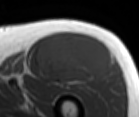
MRI of an extremity soft-tissue mass, one axial slice. Position 62 of 86 along the scan axis. MR volume resampled by the dataset authors to the PET/CT grid (not the native acquisition matrix). 139 × 117 image matrix, field of view 136 × 114 mm. Male patient. From the clinical record (not read from this slice): histological type: extraskeletal osteosarcoma; grade: high; site of the primary tumour: thigh.
Outlined on this slice (expert contour drawn on MRI and transferred to this co-registered scan by the dataset authors):
- gross tumour volume (mass): box from (x=36, y=32) to (x=112, y=85) px